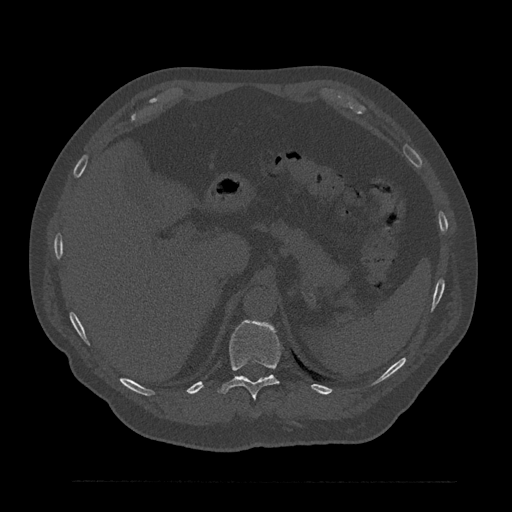
CT including the spine, one axial slice. Position 288 of 797 along the scan axis. Reconstruction kernel Br40s/3. Bone window (W 1800 / L 400 HU). 0.5 mm slice thickness. 512 × 512 image matrix, field of view 430 × 430 mm. Patient: male, 61 years. From the clinical record (not read from this slice): primary cancer: prostate.
Outlined on this slice (semi-automatic segmentation, software-assisted and operator-edited):
- T11 vertebra: bounding box (x1, y1, x2, y2) in pixels: (218, 320, 280, 399)